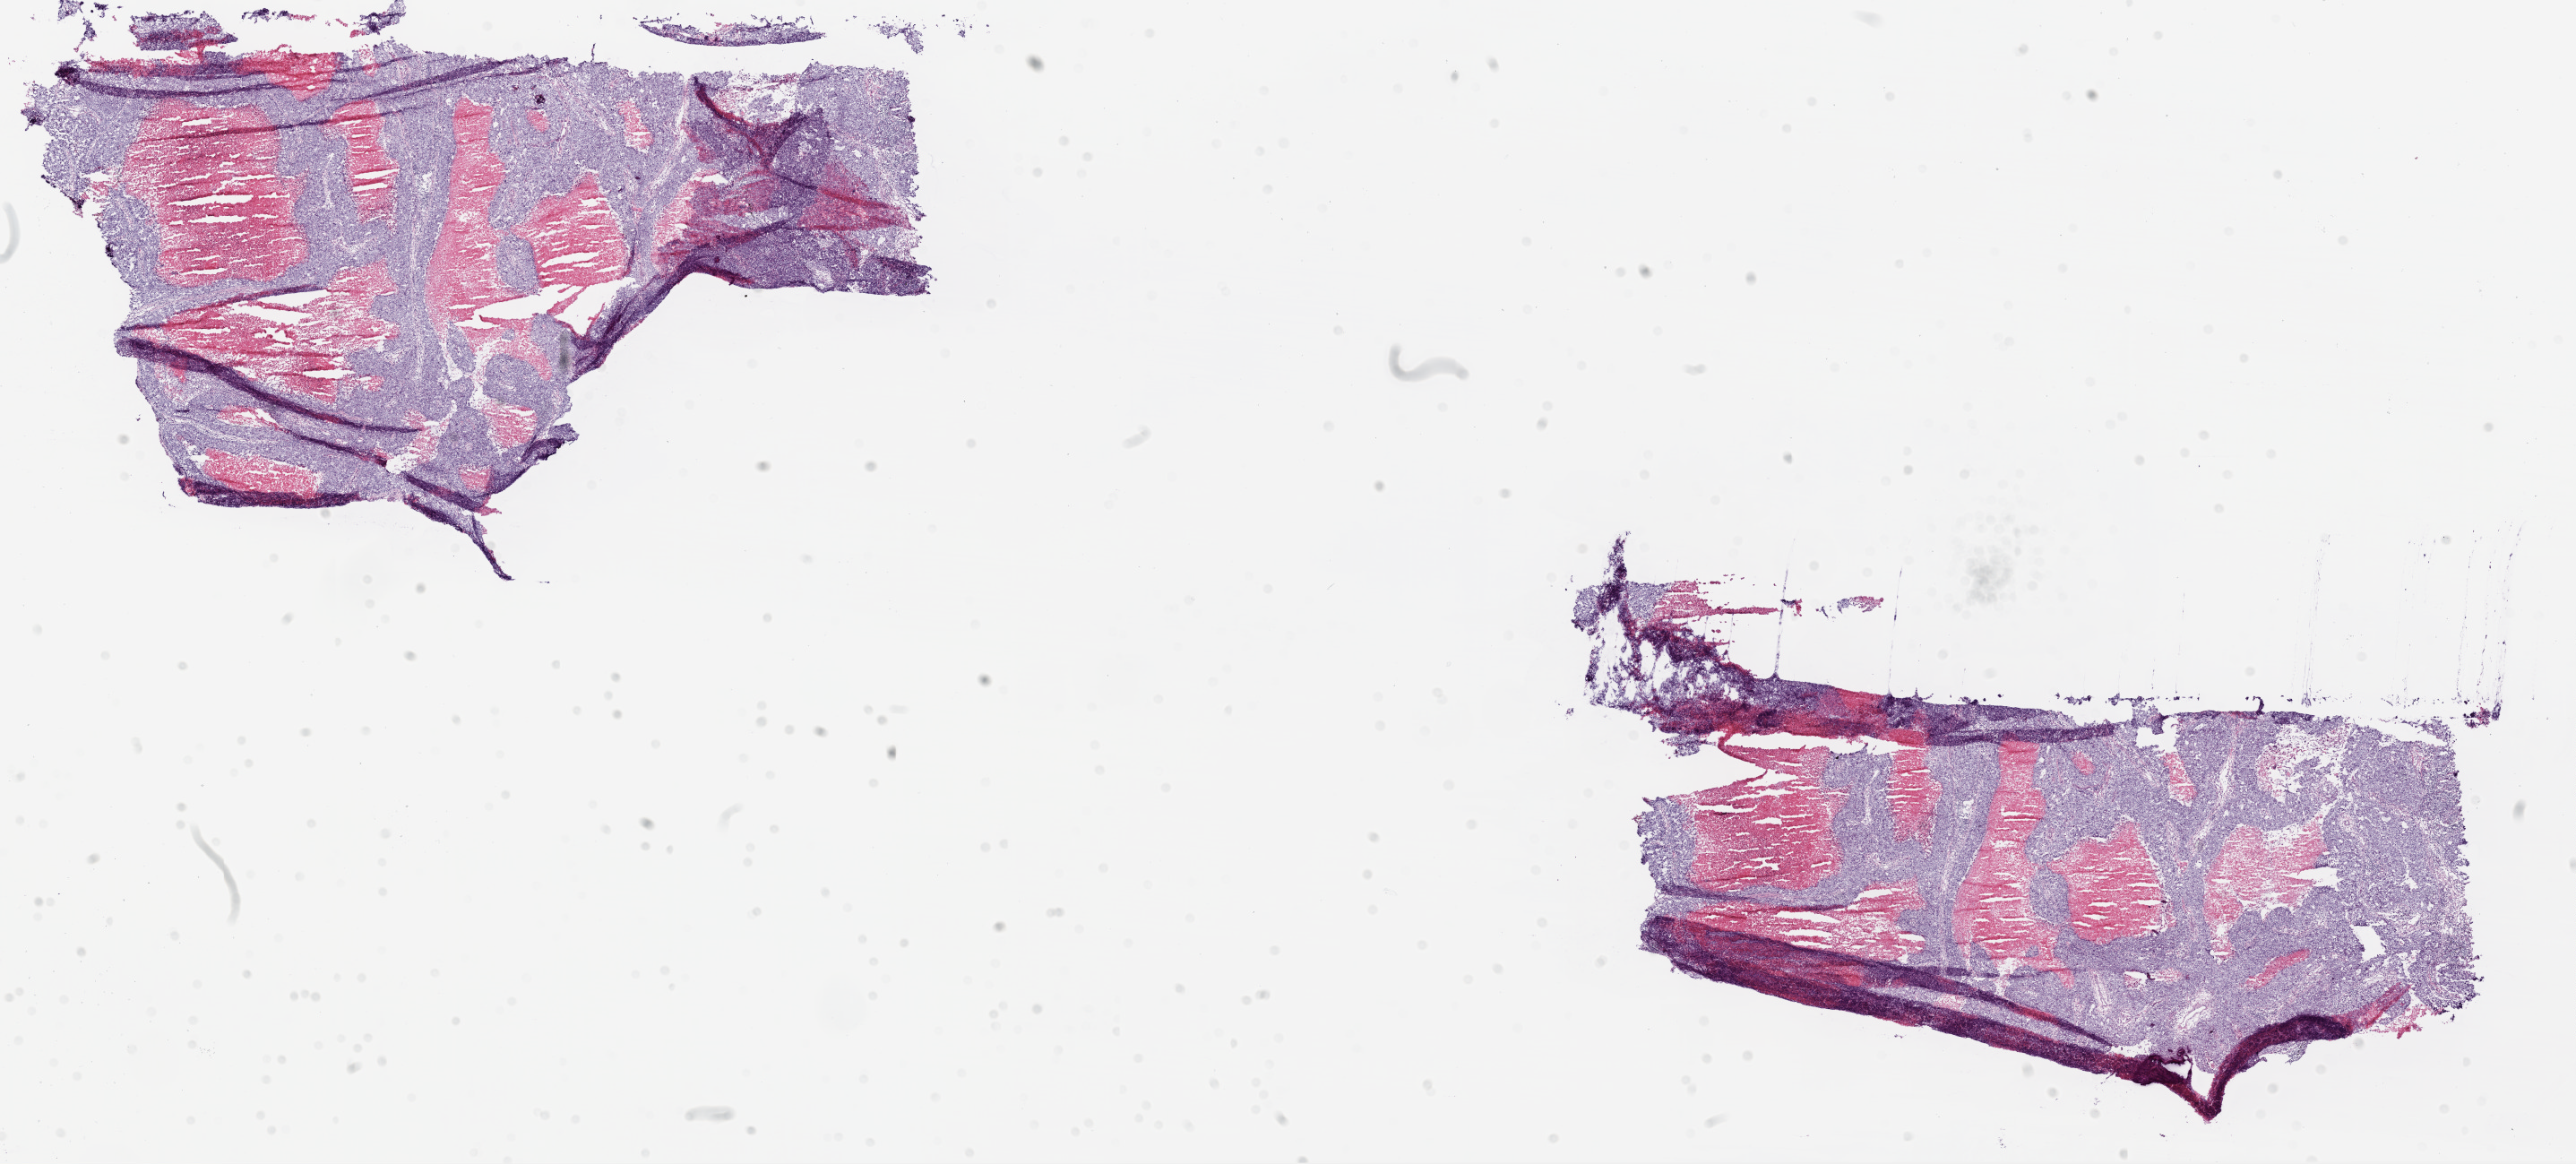
Whole-slide histology image, H&E-stained, a low-resolution overview of the entire scanned area, about 23.1 x 10.4 mm (acquisition: 20x scan); frozen section from the top of the tissue portion; sample: primary tumour, lung. Male, age 55 years at initial diagnosis. Composition of this section per pathologist review: tumour cells 75%, tumour nuclei 85%, normal cells 0%, stromal cells 5%, necrosis 20%. Inflammatory infiltration, as recorded: lymphocyte infiltration 2%.
AJCC pathologic stage: IIB (6th edition). Diagnosis: Adenocarcinoma, NOS (upper lobe, lung).